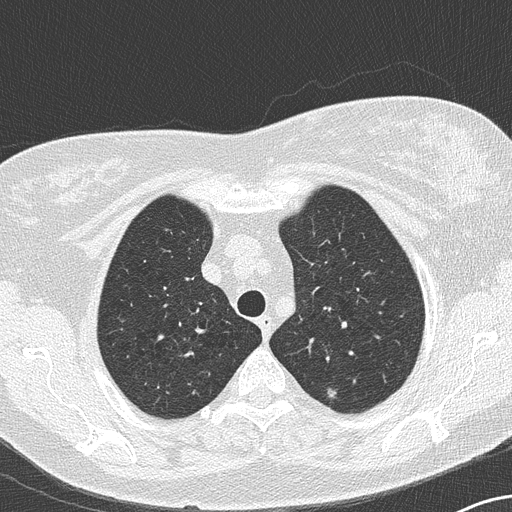
Low-dose screening chest CT, axial slice, second annual screen, lung window (W 1500 / L -600 HU), 2 mm slice thickness, lung (sharp) reconstruction kernel (B50f), 512 × 512 image matrix. Female participant, aged 65 years at enrolment. Former smoker at enrolment.
- Expert-annotated lung lesion, bounding box <307,376,351,414> (left, top, right, bottom; pixels).
- The exam's reader record, not a measurement of the box and not confirmed to be the same lesion: non-calcified nodule or mass ≥4 mm, left upper lobe, 7 × 6 mm, soft tissue attenuation, pre-existing on the prior screen: yes.
- Official screen result: positive, no significant change: stable abnormalities potentially related to lung cancer, unchanged since the prior screening exam.